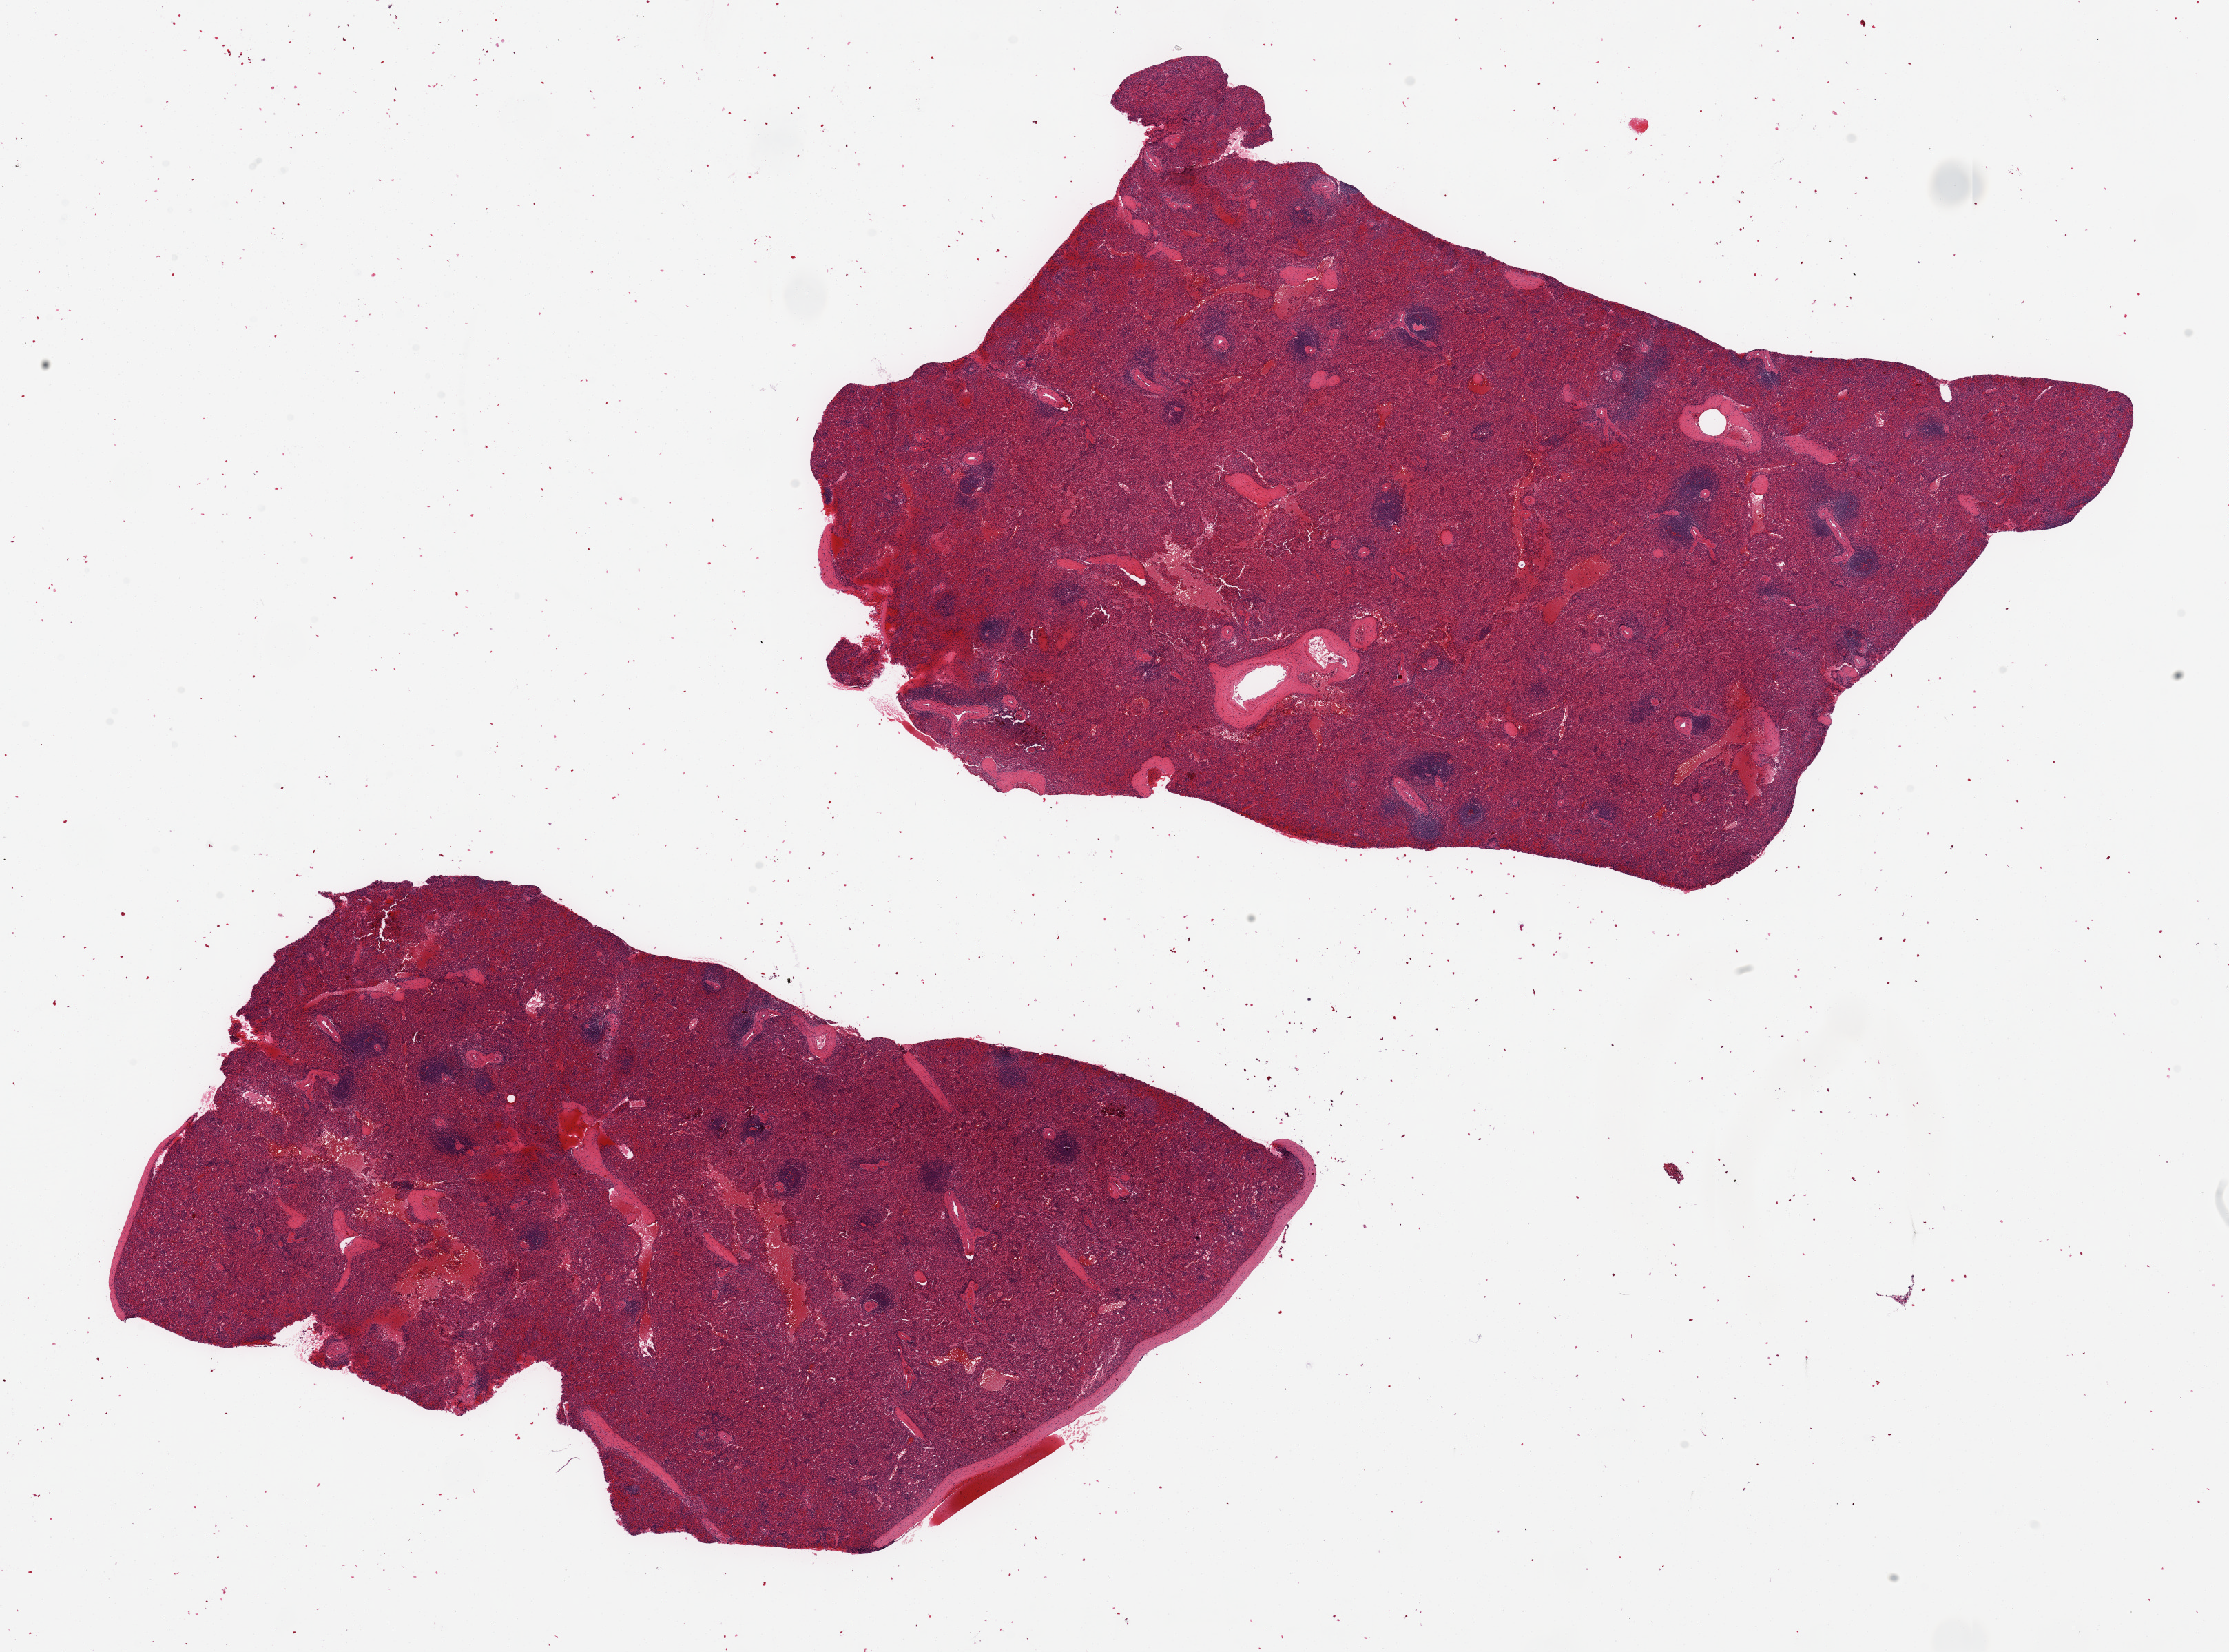
Whole-slide image, hematoxylin and eosin (H&E) stain — low-resolution overview of the scanned area, about 25.6 x 19.0 mm (acquisition: 20x scan), PAXgene-fixed paraffin-embedded (PFPE) section, target tissue: spleen, tissue donor sample.
Review note (as recorded): 2, ~11x7 mm pieces. Moderate congestion. Capsule present.